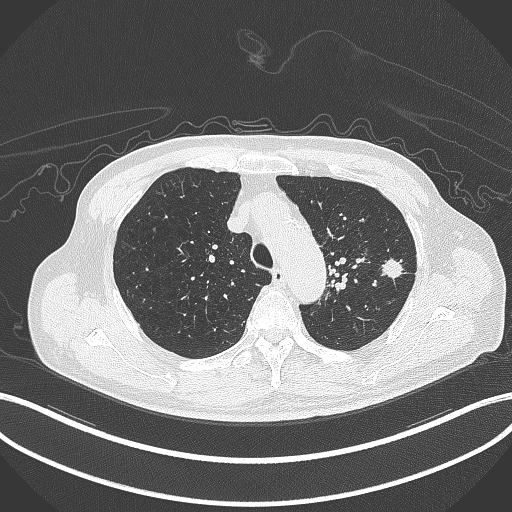
Chest CT, one axial slice; slice 338 of 417 in the series (ordered by position); reconstruction kernel B70f; lung window (W 1500 / L -600 HU); 512 × 512 image matrix. Male patient, age 77 years. From the clinical record (not read from this slice): clinical TNM (as recorded): T3 N1 M0.
Annotated regions visible in this slice (bounding box drawn by a radiologist):
- lung tumour (recorded histology: adenocarcinoma): bounding box [x1, y1, x2, y2] px = [380, 253, 404, 282]